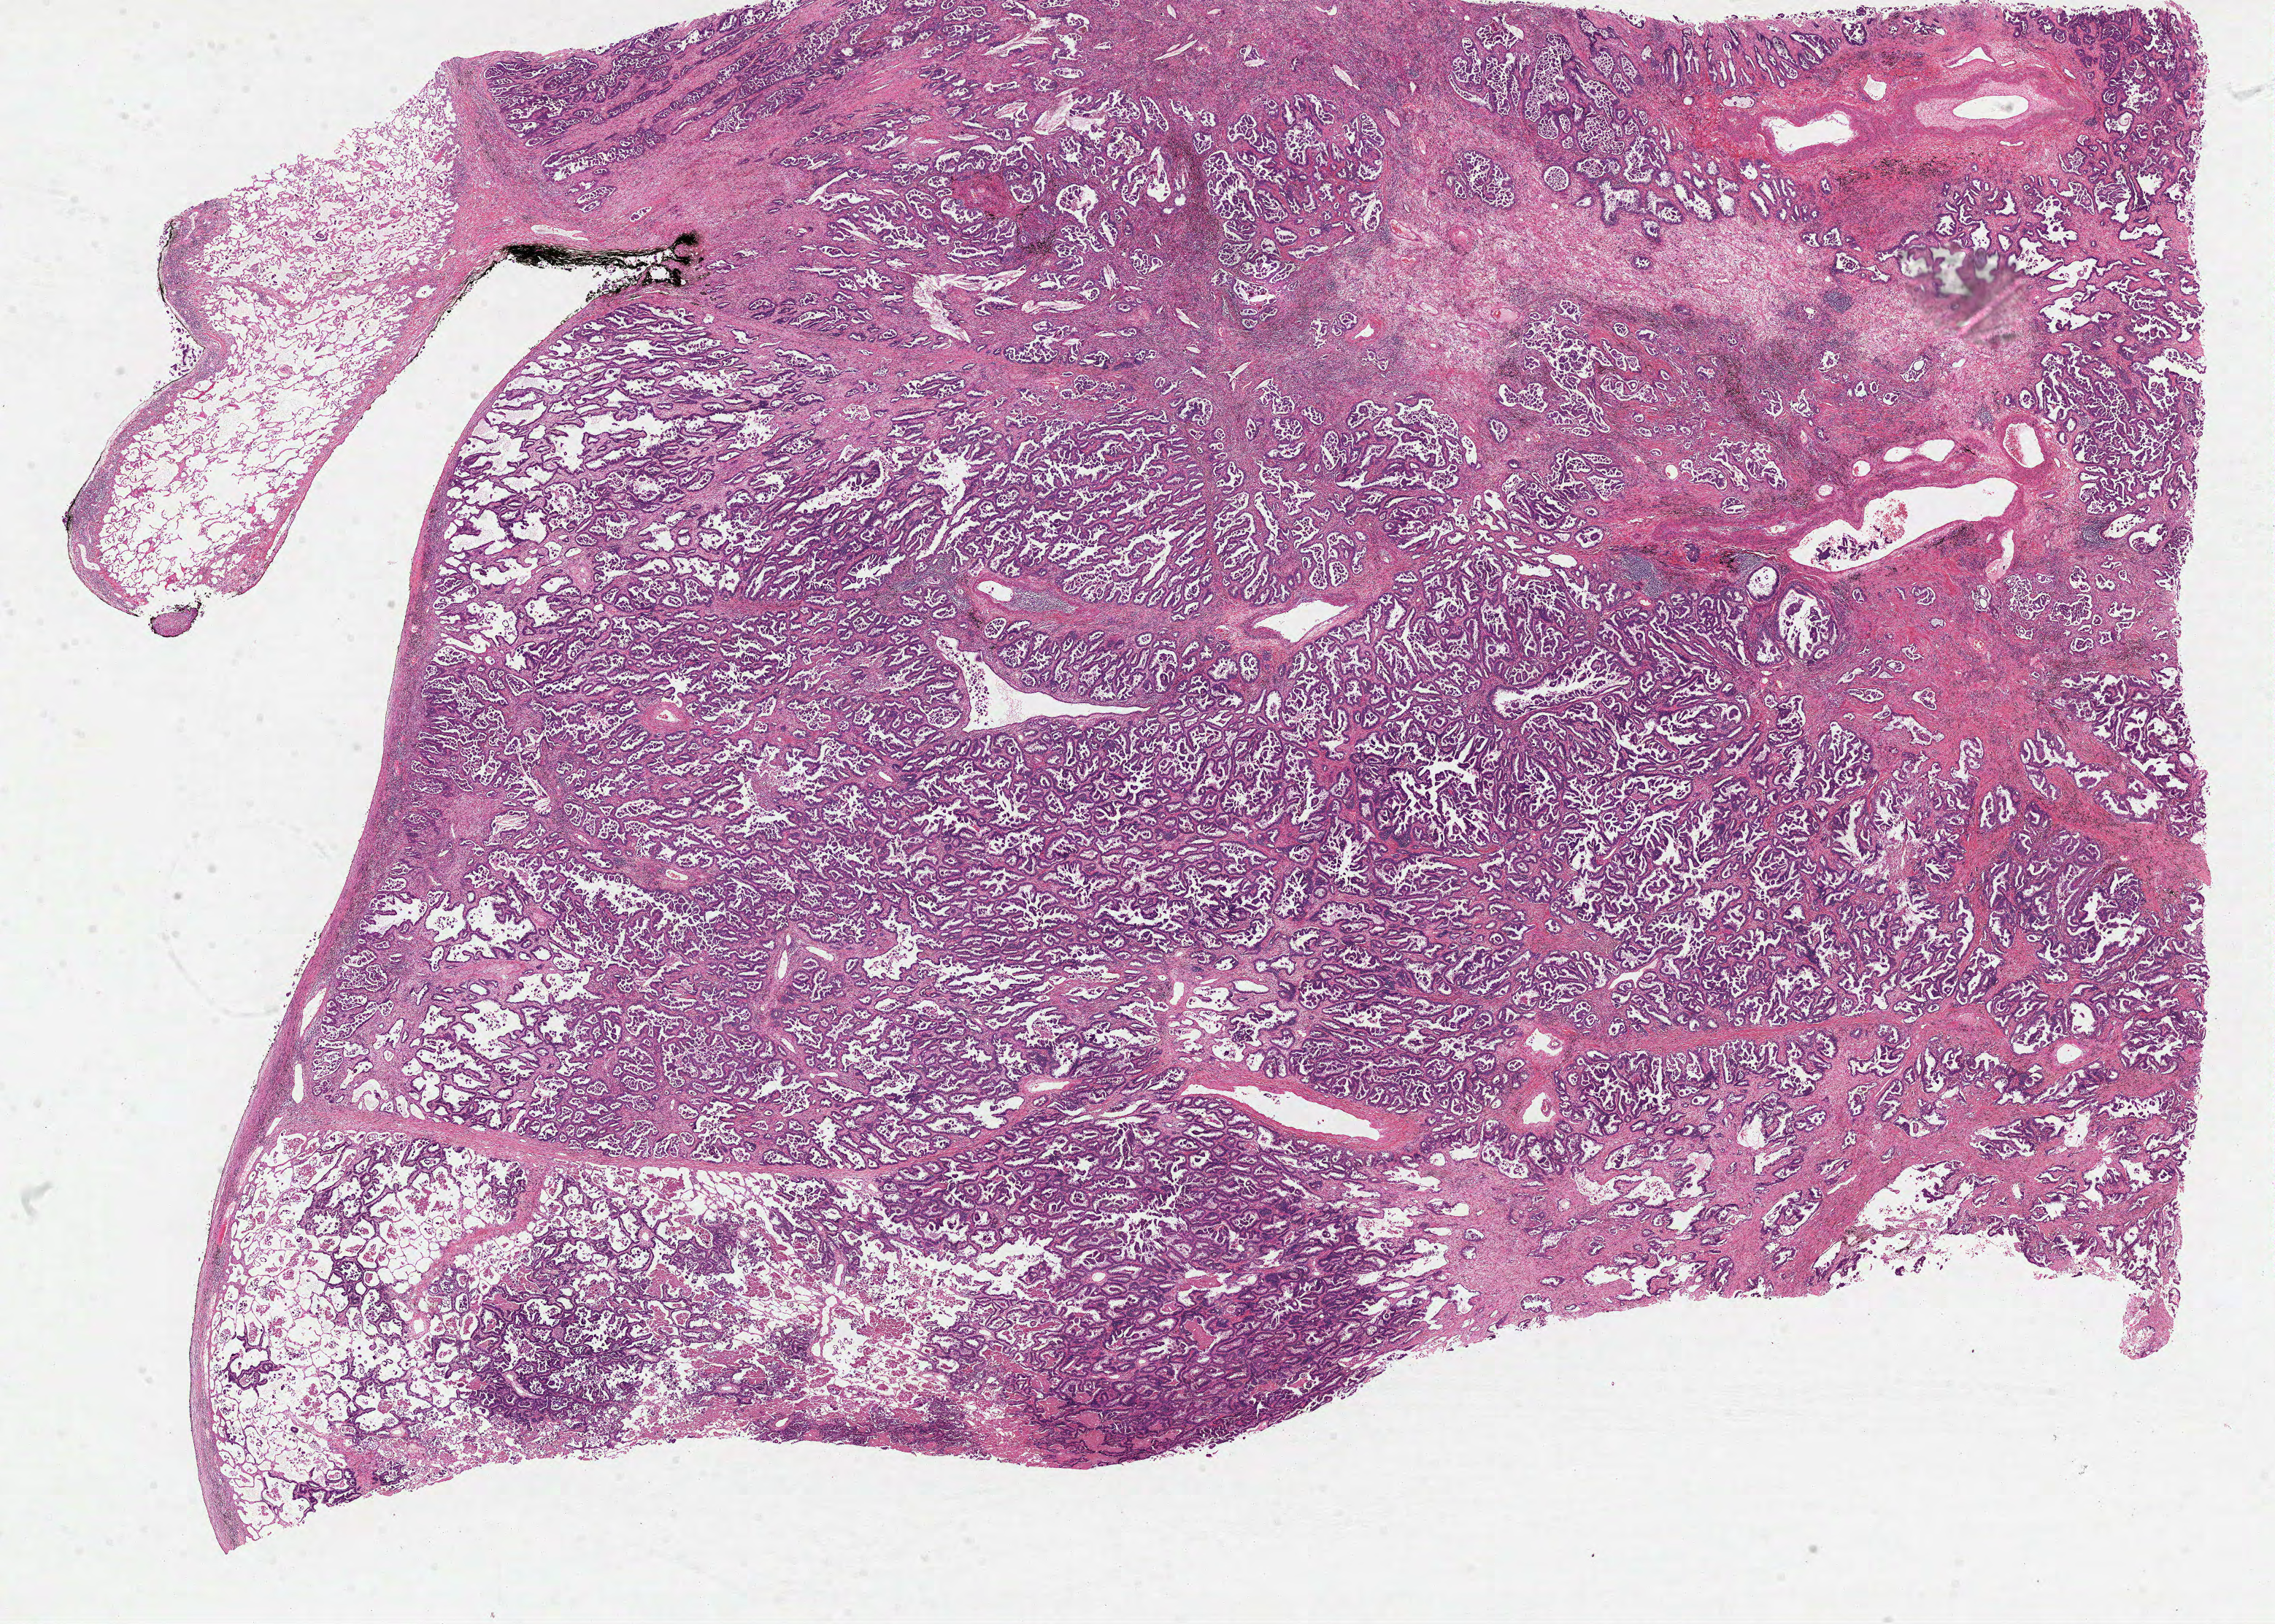
H&E whole-slide image, low-resolution overview of the scanned area, about 25.1 x 17.9 mm (acquisition: 40x scan), formalin-fixed paraffin-embedded (FFPE) diagnostic section, sample: primary tumour, lung. Female, age 59 years at initial diagnosis.
Histologic diagnosis: Adenocarcinoma with mixed subtypes (lower lobe, lung).